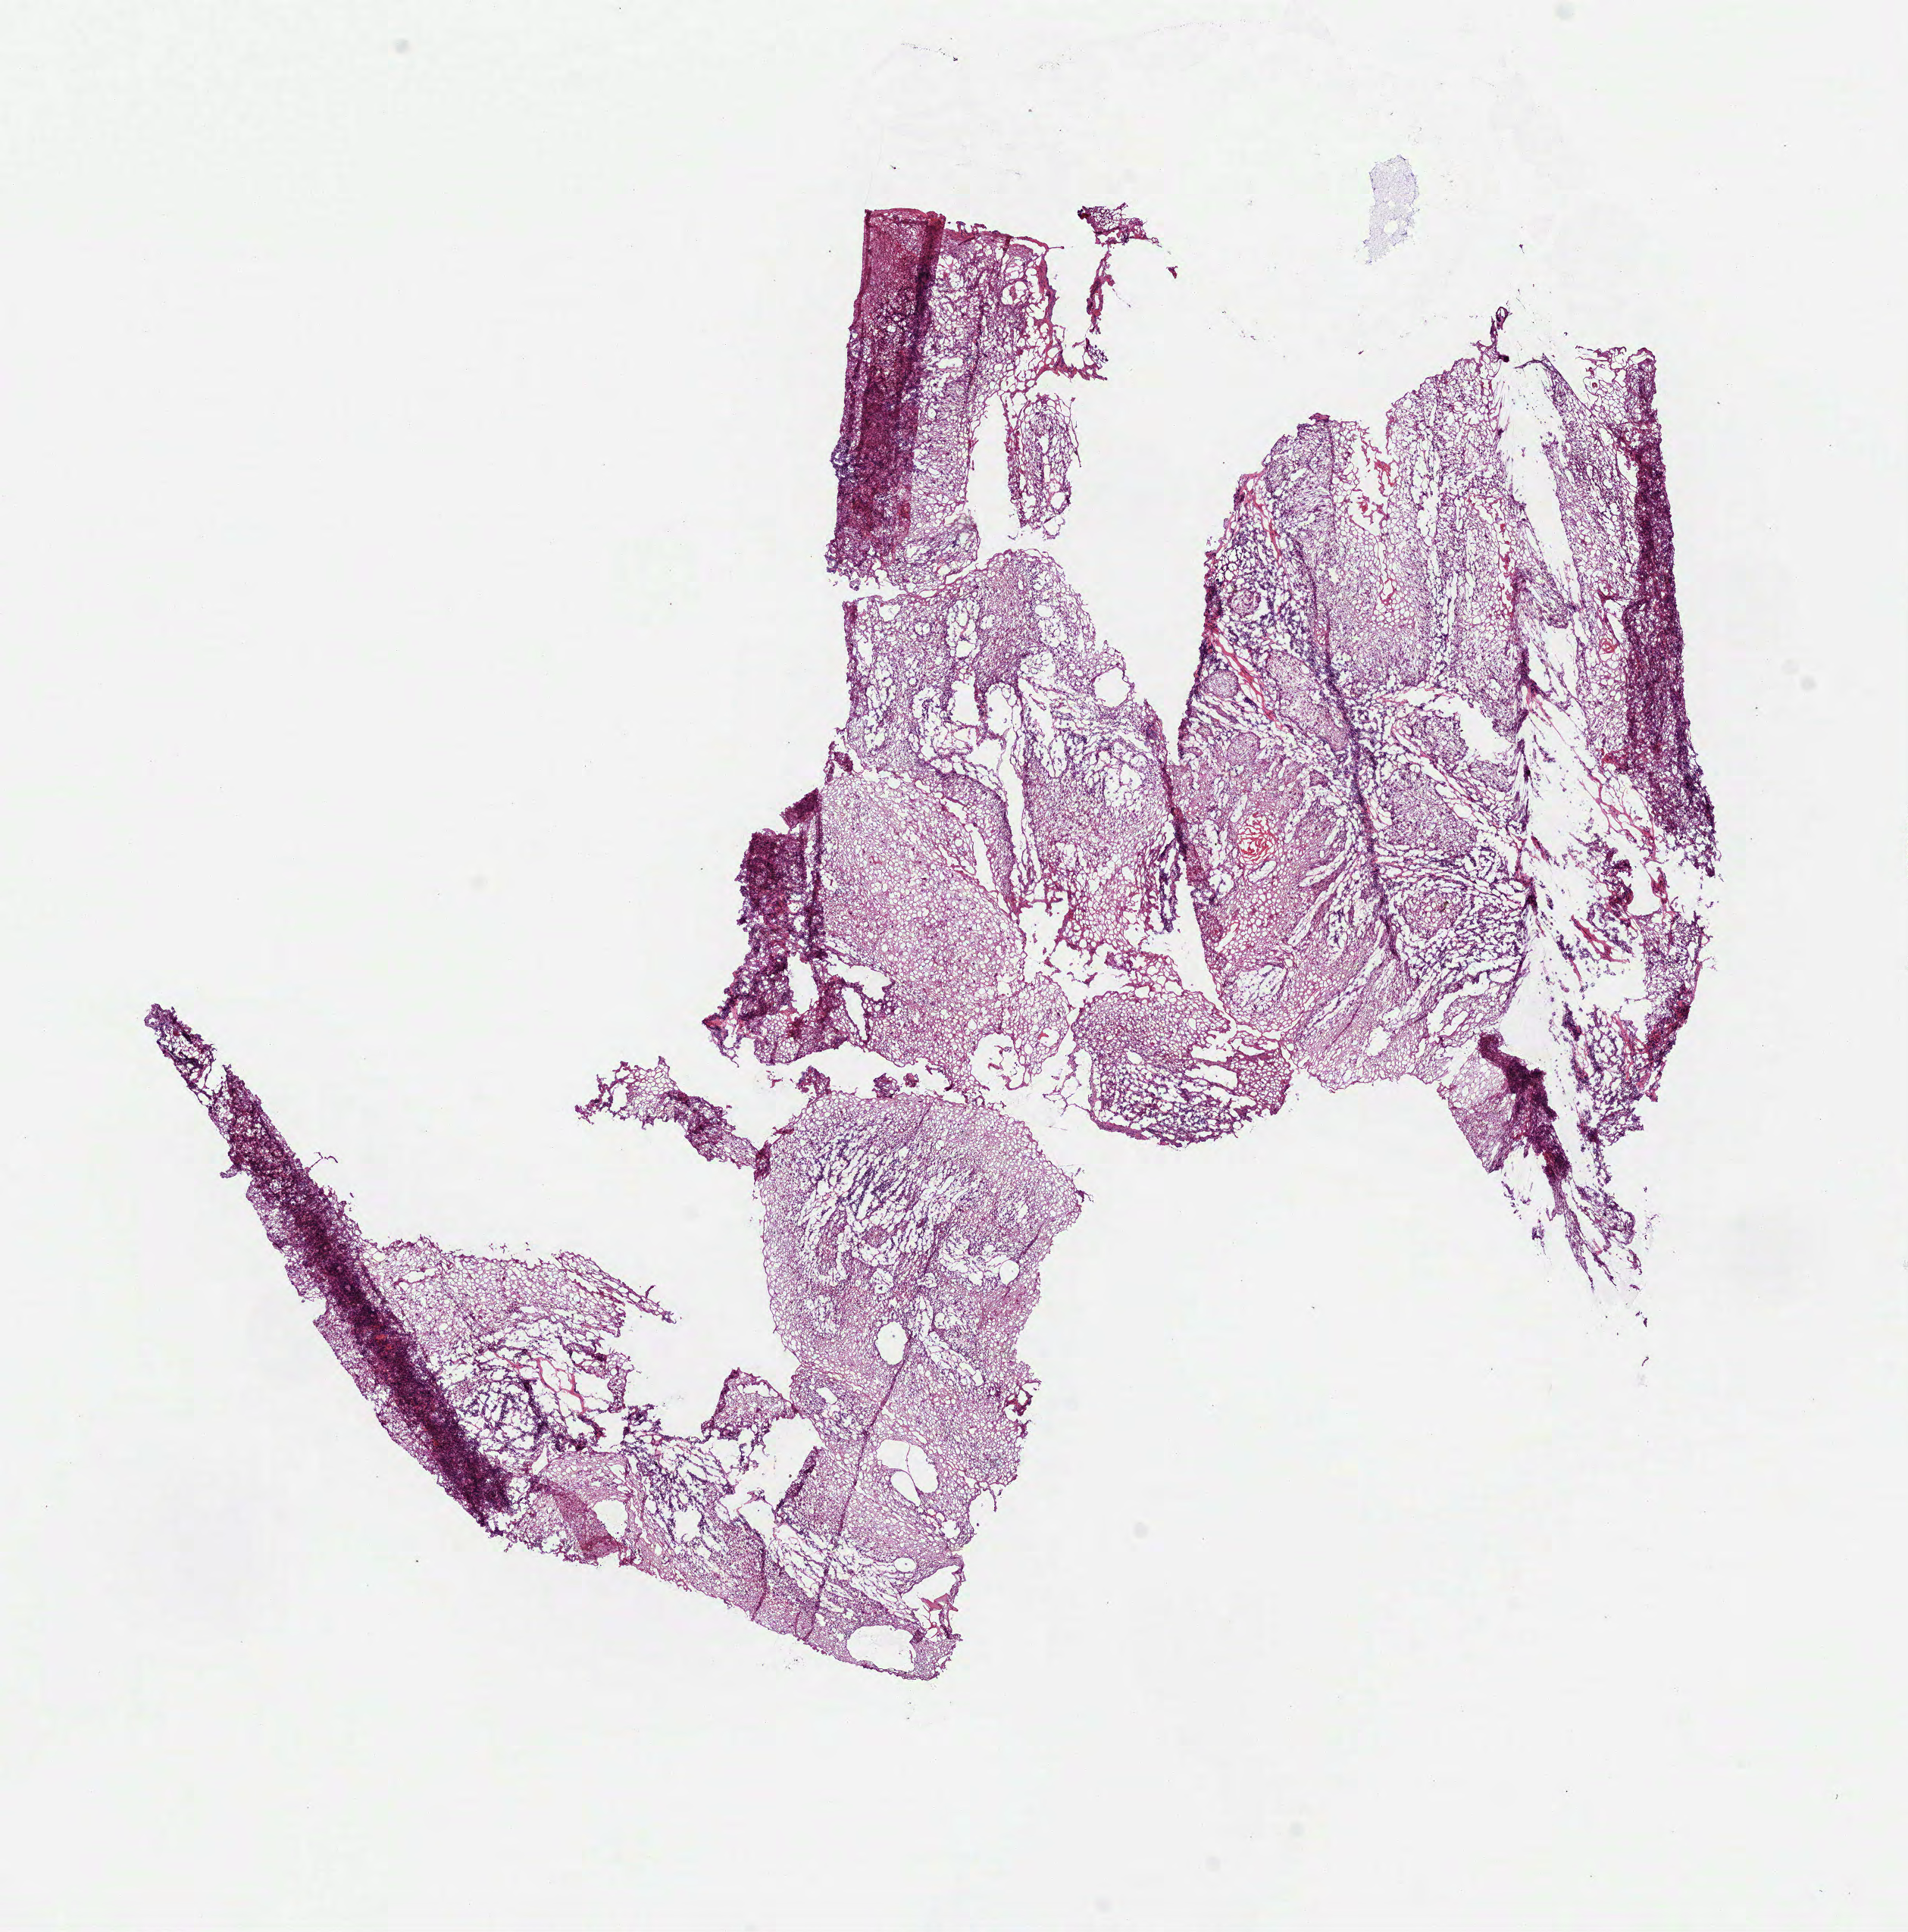
Whole-slide histology image, Hematoxylin and eosin (H&E) stained — whole scanned area (about 10.2 x 10.3 mm) shown as a low-resolution overview. Frozen section. Primary tumour sample from the head and neck. Female, age 80 years at initial diagnosis. Histologic grade: G1 (well differentiated). Composition of this section per pathologist review: tumour cells 99%, tumour nuclei 80%, normal cells 0%, stromal cells 0%, necrosis 1%. Infiltration values recorded for this section: lymphocyte infiltration 10%, monocyte infiltration 0%, neutrophil infiltration 2%.
- AJCC pathologic stage: III (7th edition)
- histologic diagnosis: Squamous cell carcinoma, NOS (floor of mouth, NOS)